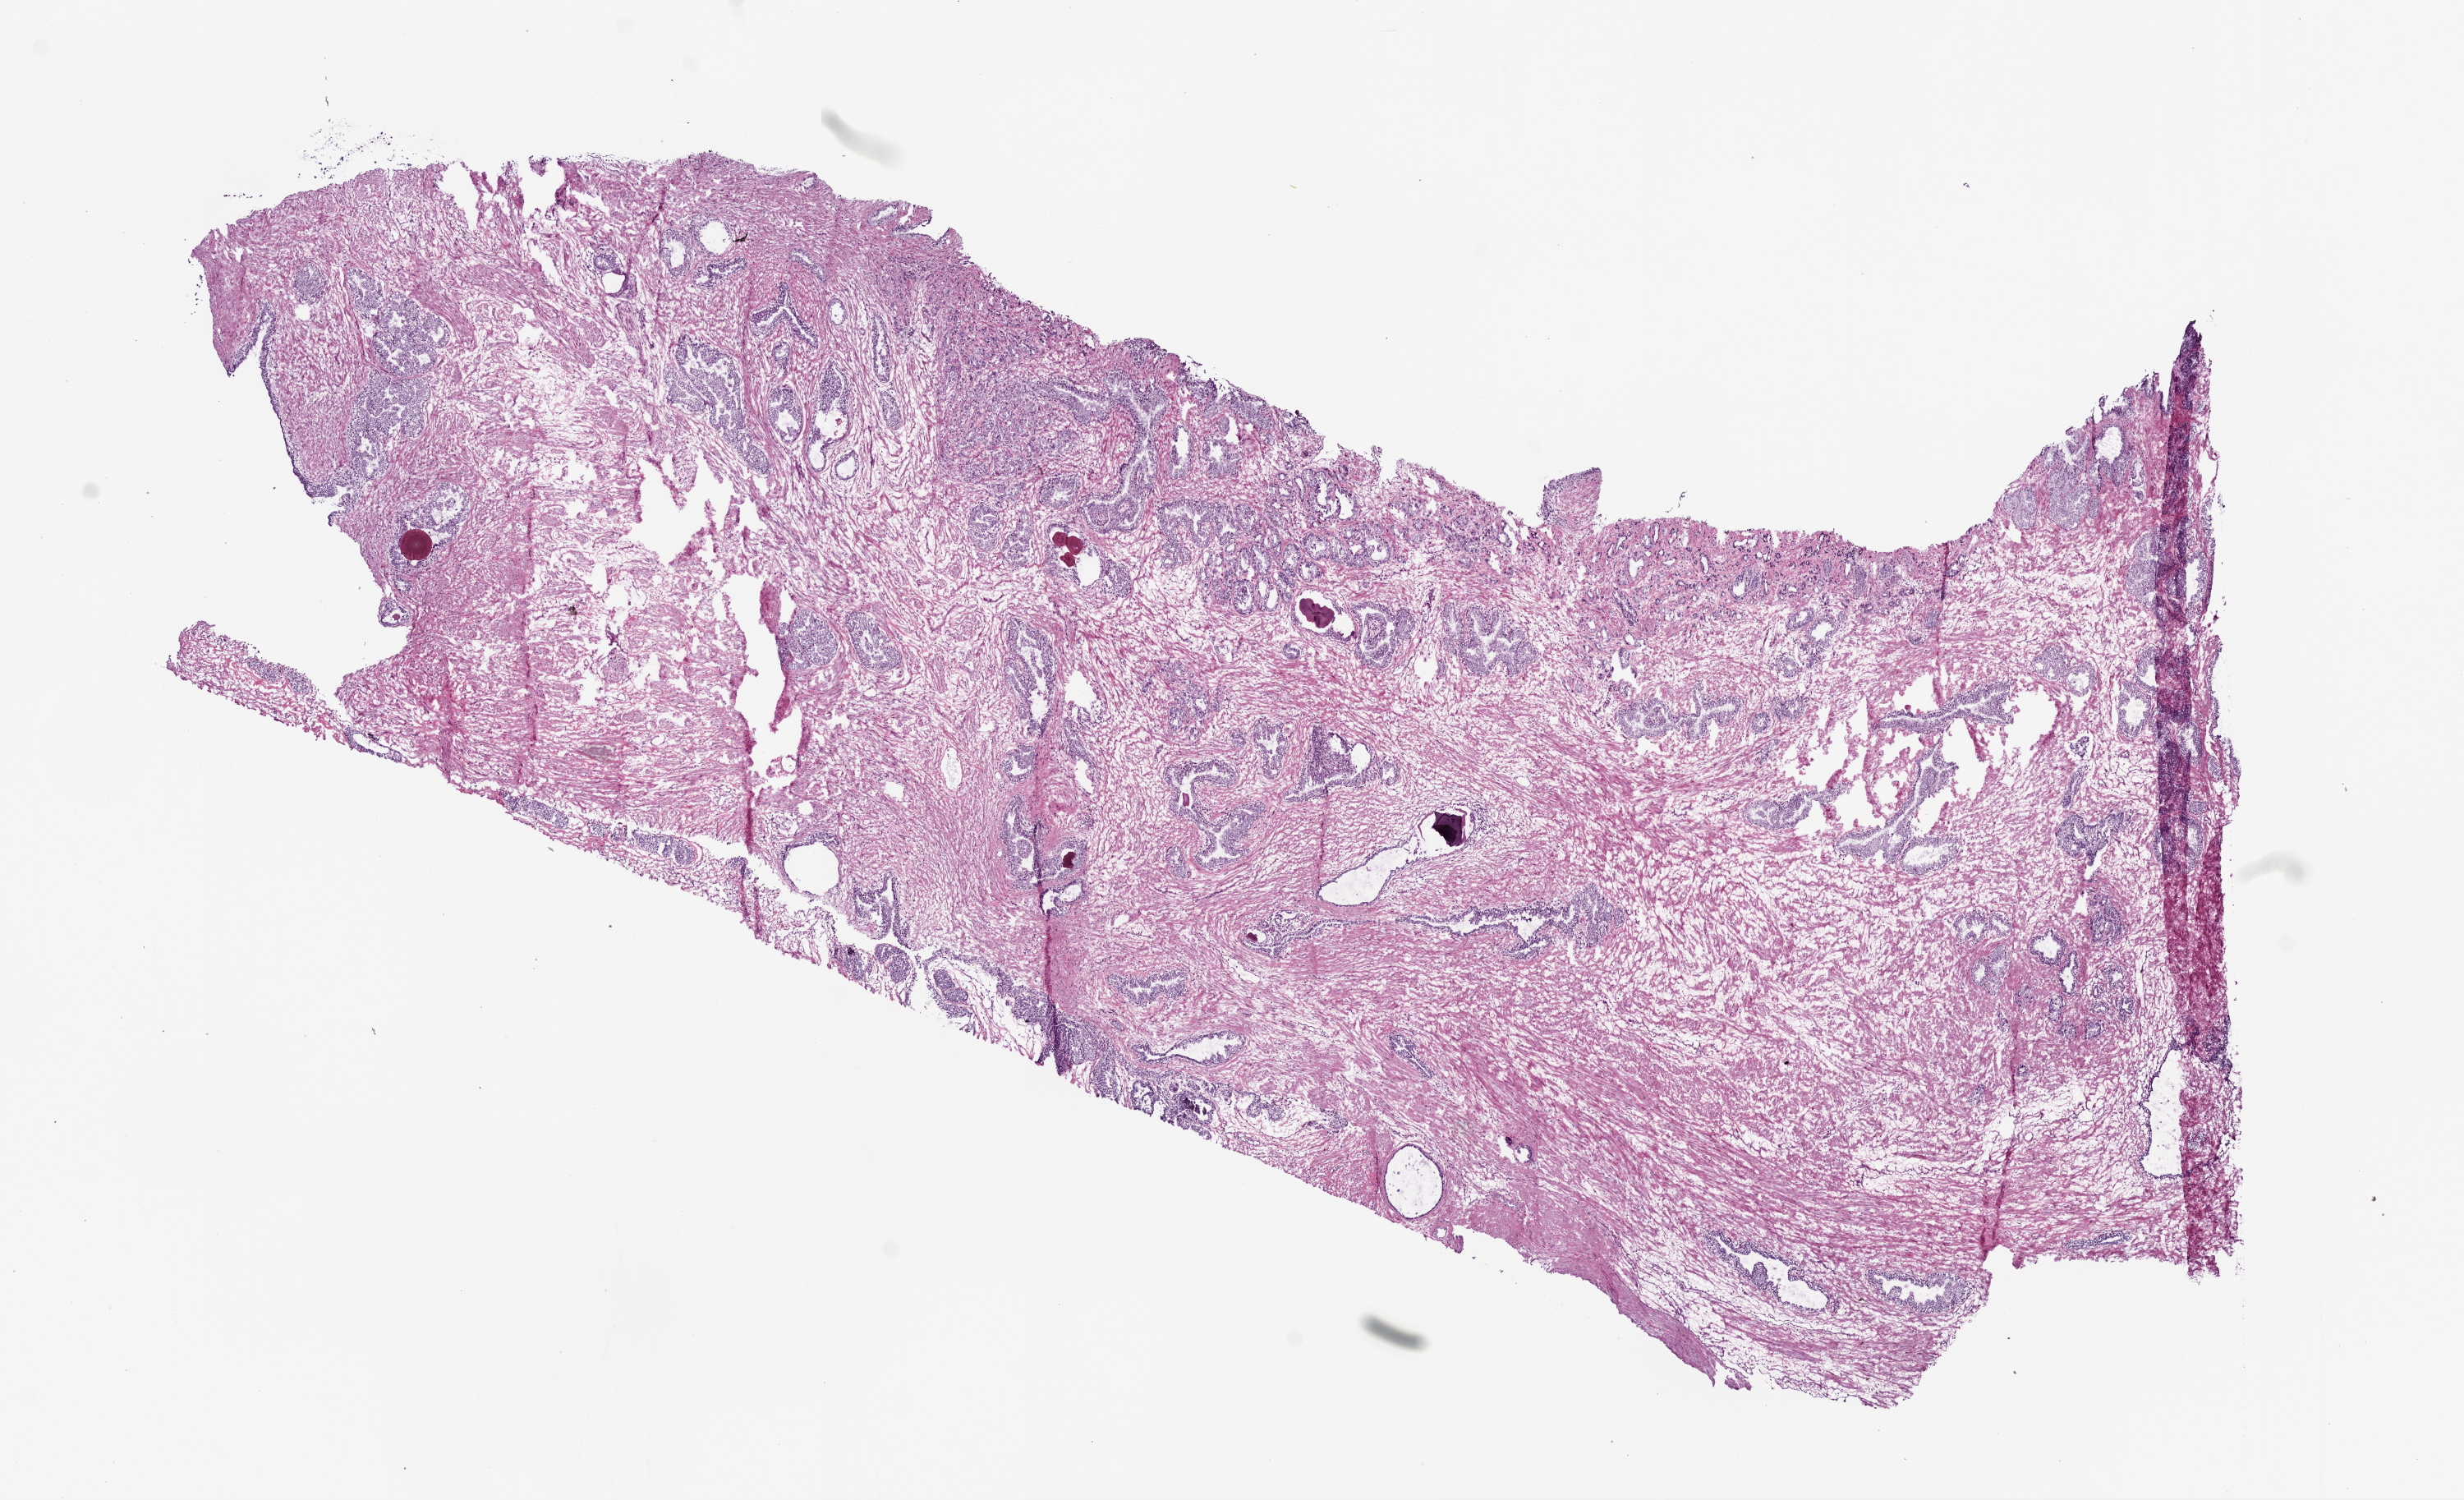
Whole-slide histology image, Hematoxylin and eosin (H&E) stained — whole scanned area (about 12.0 x 7.3 mm, slide scanned at 20x) shown as a low-resolution overview. Frozen section from the bottom of the tissue portion. Prostate, primary tumour sample. Patient: male, age at initial diagnosis 56 years. Gleason score: 7 (4+3). Pathologist review of this section (percent, as recorded): tumour cells 15%, tumour nuclei 20%, normal cells 35%, stromal cells 50%, necrosis 0%. Infiltration values recorded for this section: lymphocyte infiltration 1%, monocyte infiltration 0%, neutrophil infiltration 0%.
• diagnosis: Acinar cell carcinoma (prostate gland)
• laterality: bilateral
• lymph nodes positive (case pathology): 0 of 26 examined